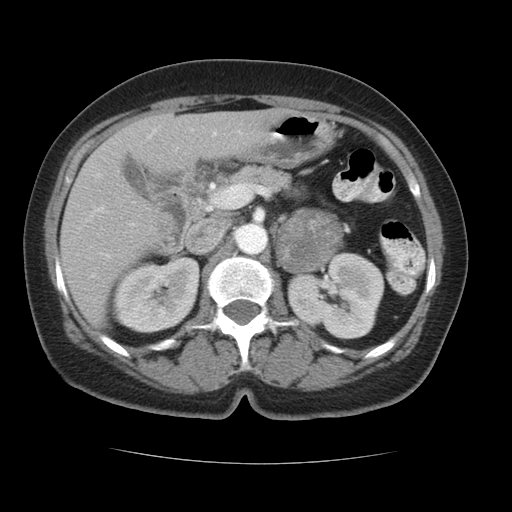
Contrast-enhanced abdominal CT, one axial slice; position 63 of 96 along the scan axis; reconstruction kernel STANDARD; intravenous contrast given; soft-tissue window (W 400 / L 40 HU); 5 mm slice thickness; 512 × 512 image matrix, field of view 348 × 348 mm. Female patient, age 66 years. Case-level facts recorded for this patient, not image findings: diagnosis: adrenocortical carcinoma; tumour side: left adrenal; tumour size at pathology: 5.5 cm; Ki-67 index: 15 %; stage (as recorded): 3.
Outlined on this slice (semi-automatically segmented with operator editing):
- mass: bounding box [x1, y1, x2, y2] px = [278, 209, 342, 270]